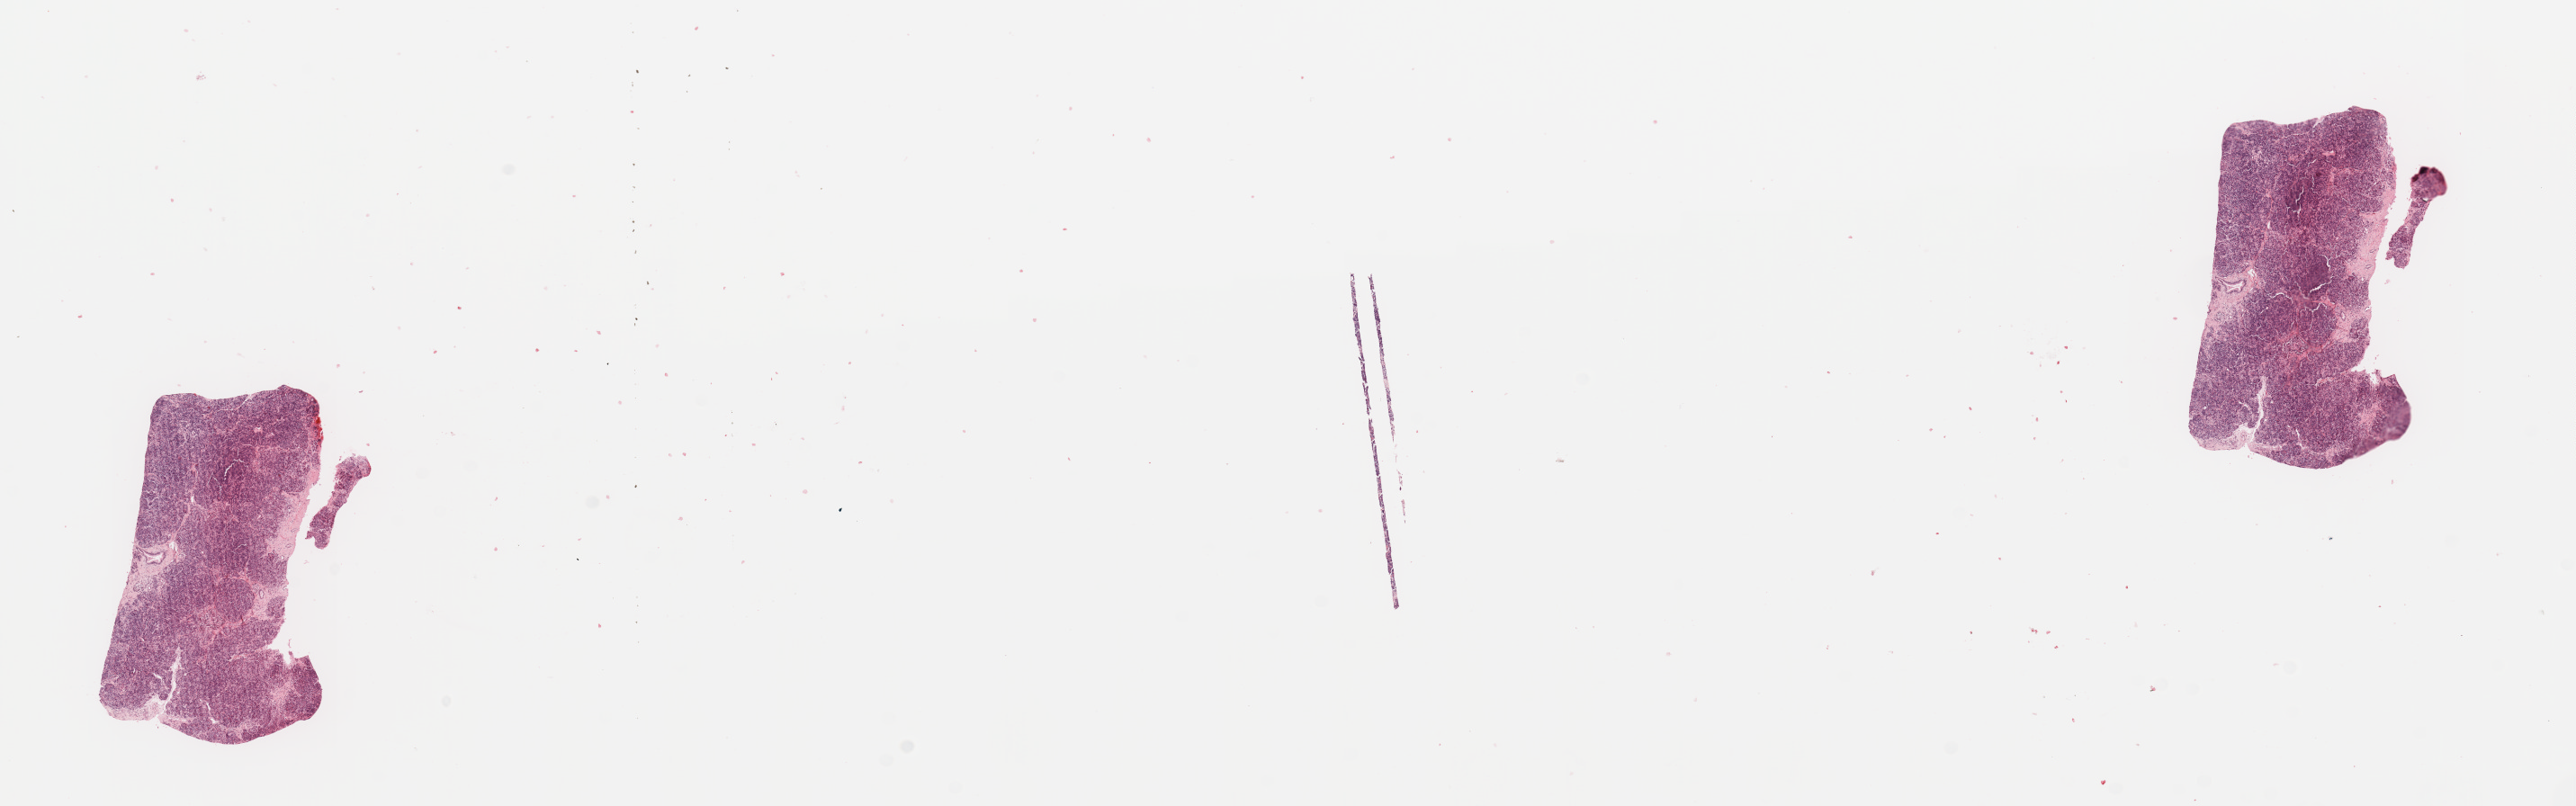
Digitized H&E-stained tissue section (whole slide) — shown as a low-resolution overview of the whole scanned area (about 22.6 x 7.1 mm), normal (non-tumour) tissue sample, pancreas. 71-year-old male patient.
This section: normal (non-tumour) tissue from the same patient. Patient diagnosis: Infiltrating duct carcinoma, NOS.